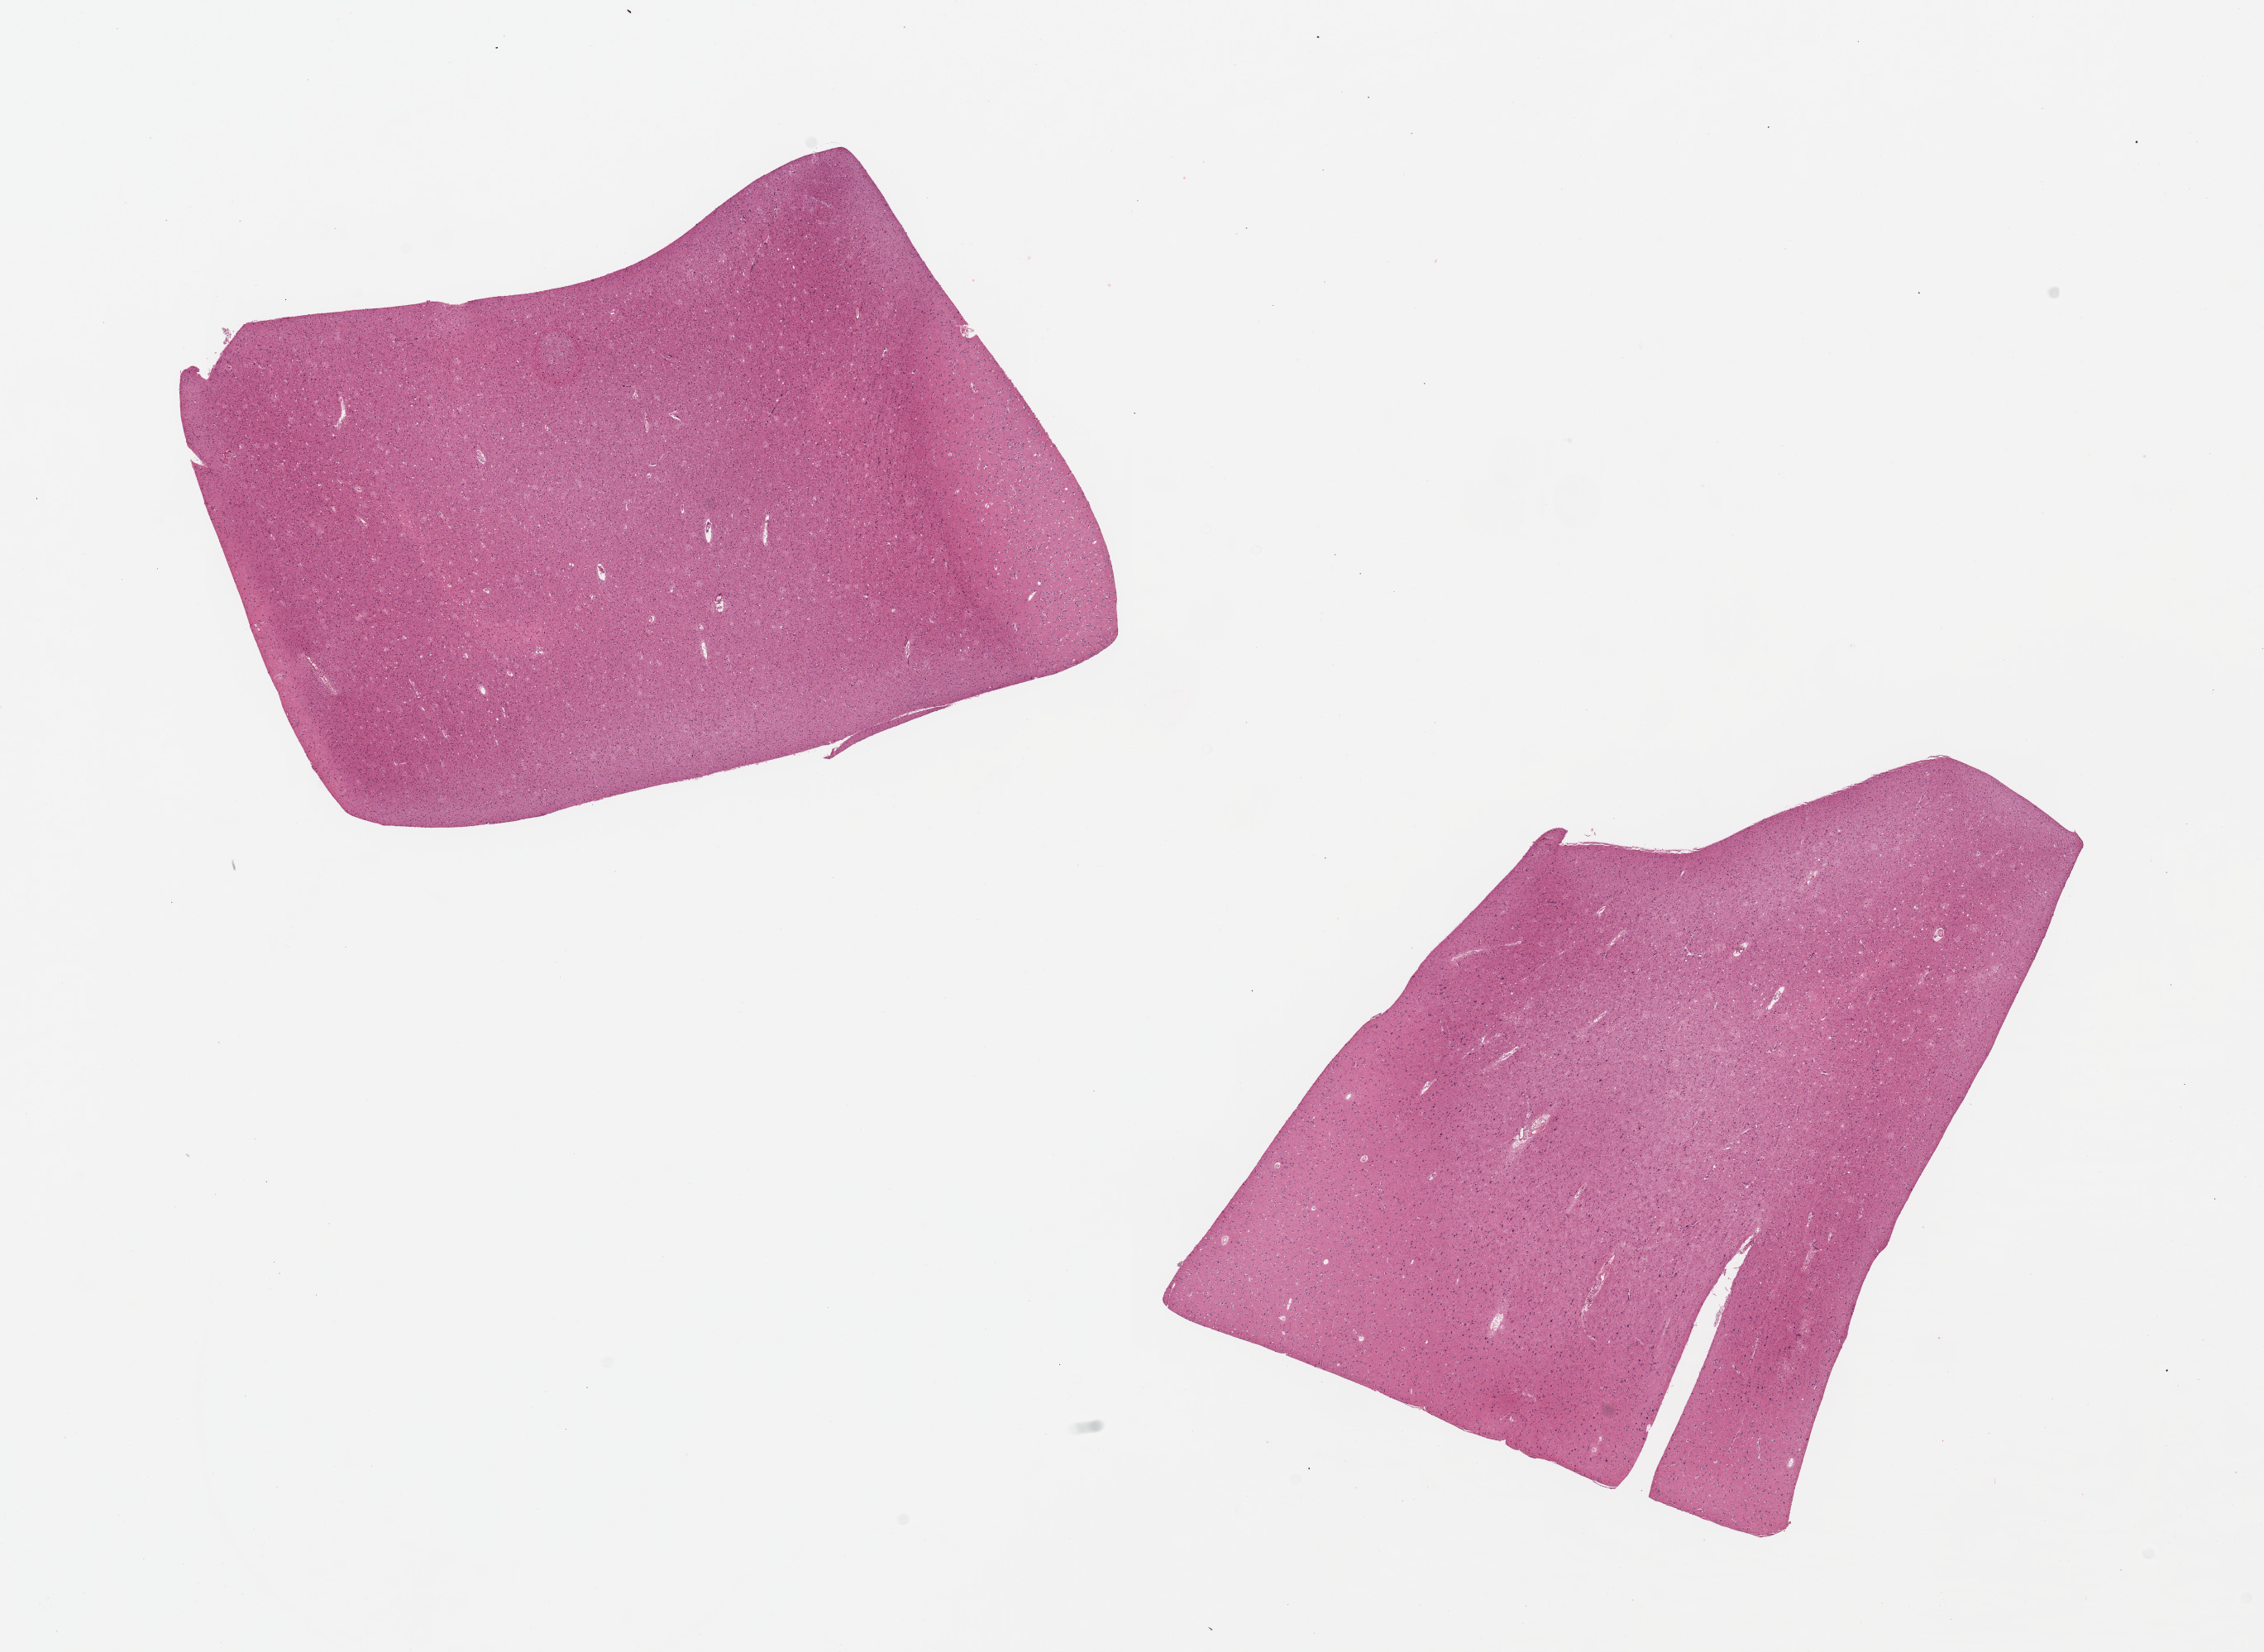
Whole-slide image, H&E stain, shown as a low-resolution overview of the whole scanned area (about 21.7 x 15.8 mm), PAXgene-fixed paraffin-embedded (PFPE) section, target tissue: cerebral cortex, donor tissue sample.
Pathologist's review note for this sample: 2 pieces; more white matter than usual.